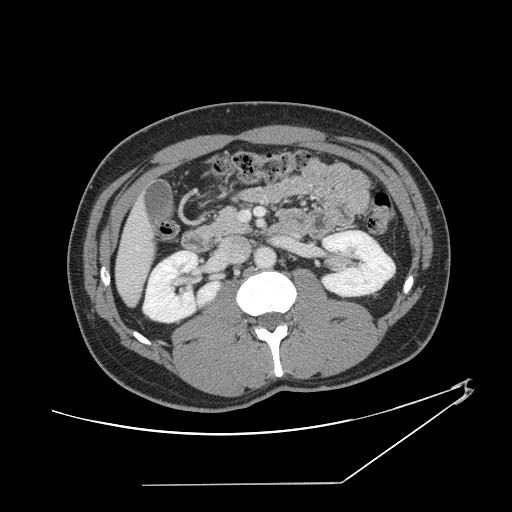
Contrast-enhanced abdominal CT, one axial slice; position 54 of 152 along the scan axis; reconstruction kernel STANDARD; 120 kVp; intravenous contrast given; soft-tissue window (W 400 / L 40 HU); 2.5 mm slice thickness; 512 × 512 image matrix. Male patient, age 45 years. Case-level facts recorded for this patient, not image findings: diagnosis: colorectal cancer liver metastases, imaged before liver resection.
Outlined on this slice (expert manual segmentation):
- hepatic veins: bounding box <135,246,140,251> (left, top, right, bottom; pixels)
- liver: <117,204,152,304>
- planned liver remnant (the part of the liver to remain after resection): <117,204,152,304>
- portal vein (with intrahepatic branches): <241,208,264,221>